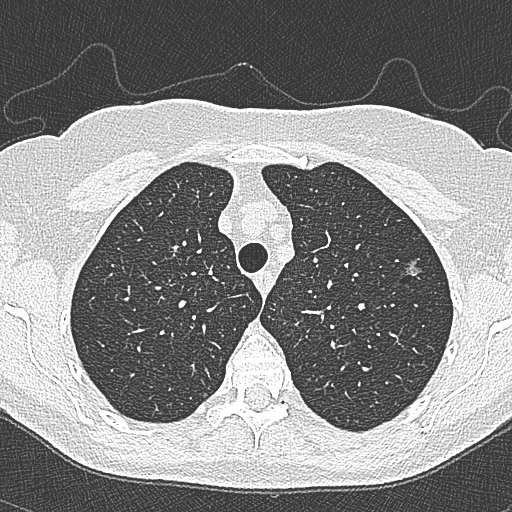
Low-dose screening chest CT, axial slice, second annual screen, lung window (W 1500 / L -600 HU), 120 kVp, slice 71 of 350 in the series. Female participant, aged 65 years at enrolment. Current smoker at enrolment.
- Expert-annotated lung lesion, bounding box [x1, y1, x2, y2] px = [395, 251, 433, 288].
- The screening reader recorded 4 non-calcified nodules or masses ≥4 mm on this exam (left upper lobe, left upper lobe, left upper lobe, right lower lobe); which of them this box marks is not recorded.
- Lung cancer was diagnosed 54 days after this screen: bronchiolo-alveolar carcinoma, non-mucinous, left upper lobe, stage IA (AJCC 6th edition), 10 mm at pathology.